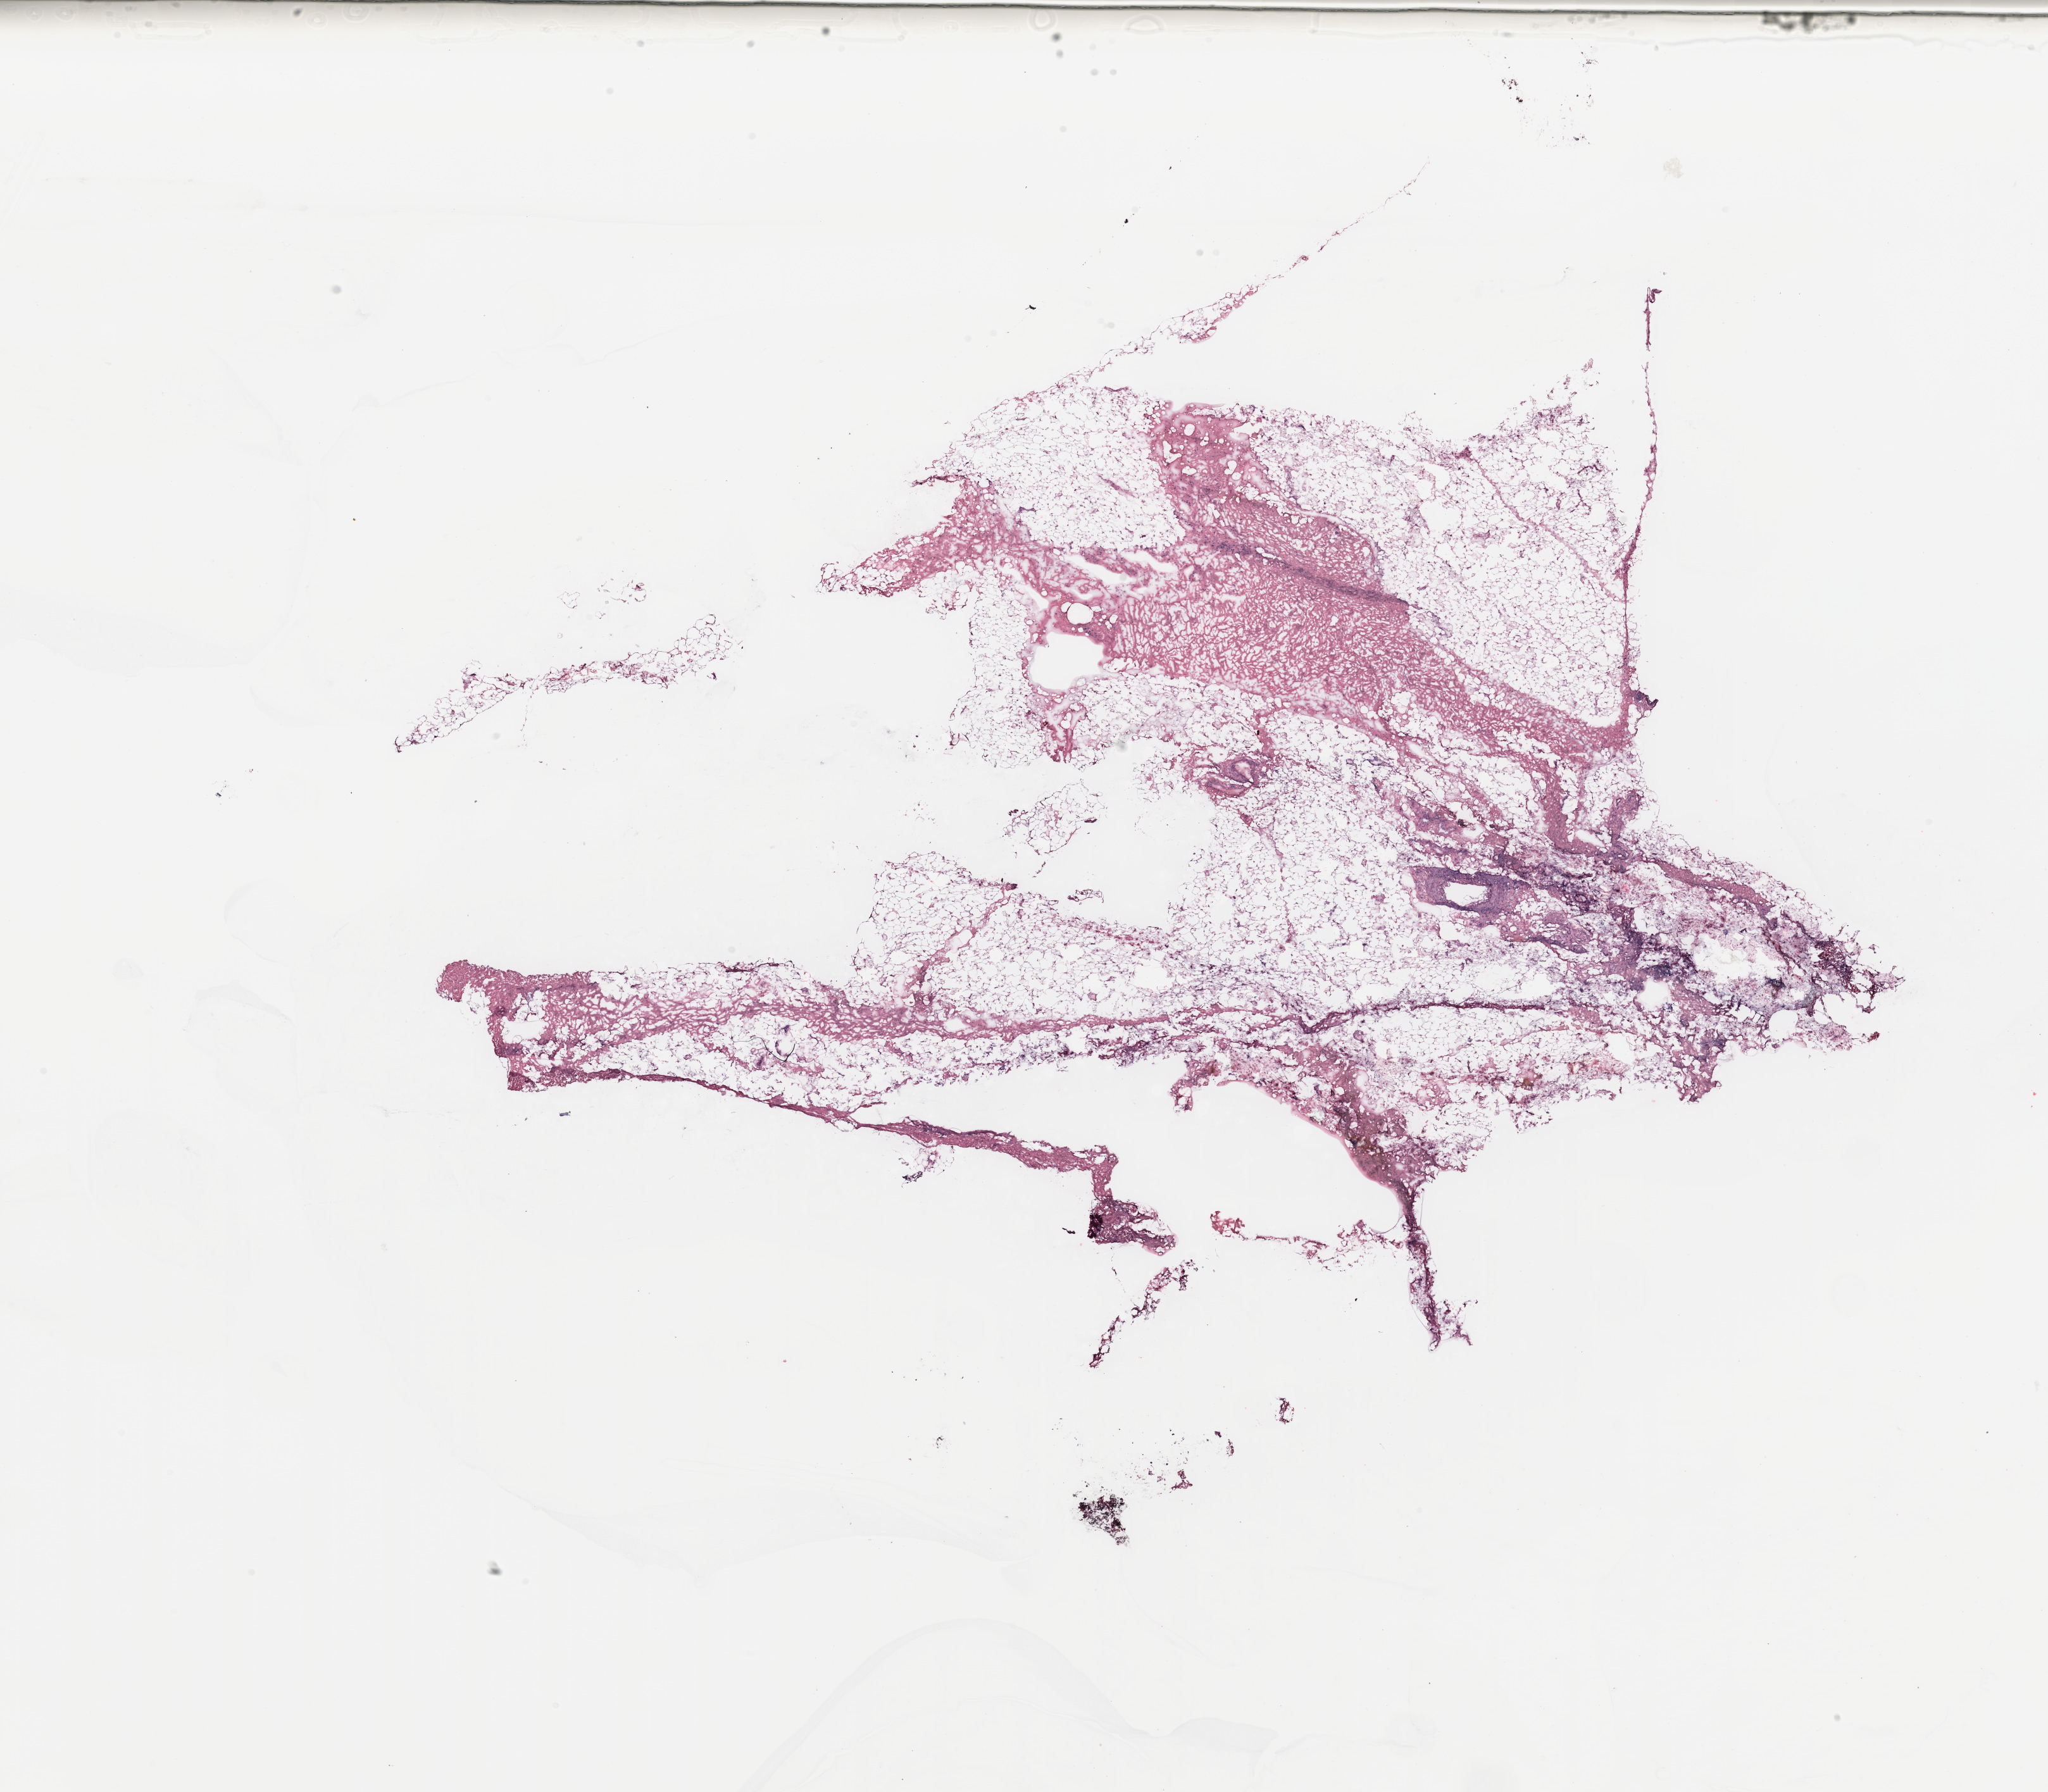
Digitized H&E-stained tissue section (whole slide), a low-resolution overview of the entire scanned area, about 25.6 x 22.4 mm (from a 20x scan). Breast, tumour tissue. Female, 65 y/o.
Histologic diagnosis: Infiltrating duct carcinoma, NOS. AJCC pathologic stage: IIA.